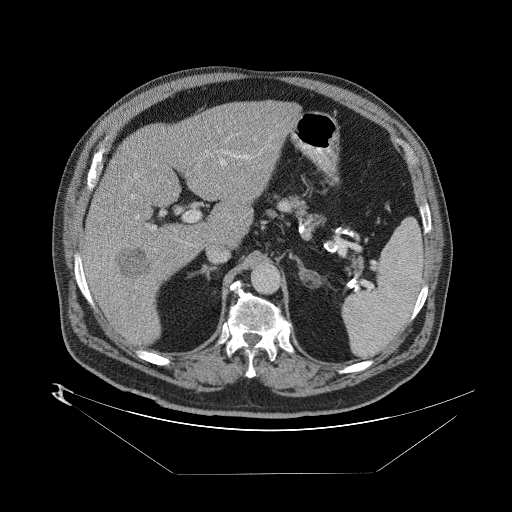
Contrast-enhanced abdominal CT (liver protocol), one axial slice. Slice 47 of 89 in the series (ordered by position). Reconstruction kernel STANDARD. One of 2 acquisitions stored at this slice position. Soft-tissue window (W 400 / L 40 HU). 2.5 mm slice thickness. 512 × 512 image matrix, field of view 480 × 480 mm. From the clinical record (not read from this slice): diagnosis: hepatocellular carcinoma (patient treated with transarterial chemoembolisation; whether this scan precedes or follows treatment is not stated here); TNM stage (as recorded): Stage-II; Child-Pugh class: B; tumour differentiation: moderately differentiated.
Structures marked on this image (semi-automatic segmentation, software-assisted and operator-edited):
- abdominal aorta: bounding box (x1, y1, x2, y2) in pixels: (251, 263, 280, 292)
- liver parenchyma outside the tumour (the mass and vessels are separate outlines, so this box may not span the whole liver): (84, 98, 297, 346)
- mass: (113, 243, 153, 283)
- liver vessels: (91, 132, 285, 304)